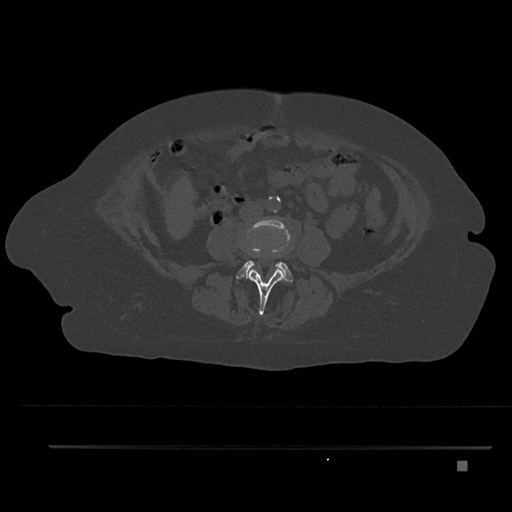
CT including the spine, one axial slice; position 105 of 797 along the scan axis; reconstruction kernel Br40s/3; 120 kVp; bone window (W 1800 / L 400 HU); 0.5 mm slice thickness; 512 × 512 image matrix. Patient: female, 76 years. Case-level facts recorded for this patient, not image findings: primary cancer: lung; vertebrae with lytic lesions (as recorded): T11, L3.
Structures marked on this image (semi-automatically segmented with operator editing):
- L3 vertebra: bounding box <249,266,285,315> (left, top, right, bottom; pixels)
- L4 vertebra: <236,220,293,282>